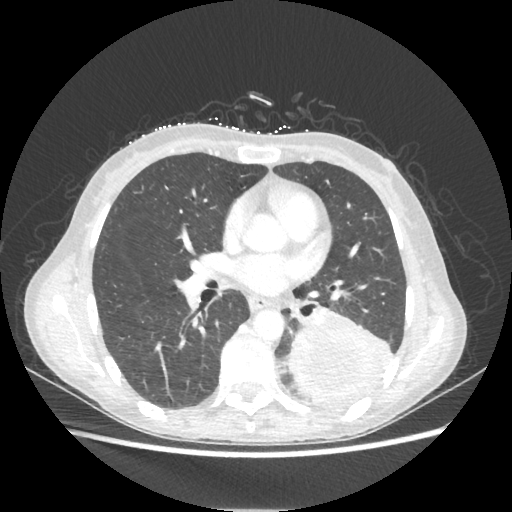
Chest CT, one axial slice. Position 111 of 221 along the scan axis. Lung window (W 1500 / L -600 HU). 1.25 mm slice thickness. 512 × 512 image matrix, field of view 360 × 360 mm. Patient: female, 53 years. From the clinical record (not read from this slice): clinical TNM (as recorded): T3 N0 M0.
Structures marked on this image (rectangle marked by the reading radiologist):
- lung tumour (recorded histology: adenocarcinoma): bounding box (x1, y1, x2, y2) in pixels: (290, 308, 395, 409)